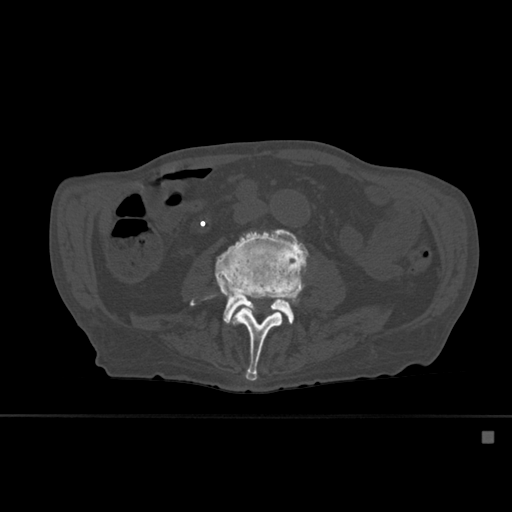
CT including the spine, one axial slice. Bone window (W 1800 / L 400 HU). 512 × 512 image matrix. Male patient, age 78 years. From the clinical record (not read from this slice): primary cancer: prostate.
Outlined on this slice (semi-automatic segmentation, software-assisted and operator-edited):
- L3 vertebra: box from (x=227, y=259) to (x=302, y=381) px
- L4 vertebra: (x=190, y=228)–(x=309, y=324)